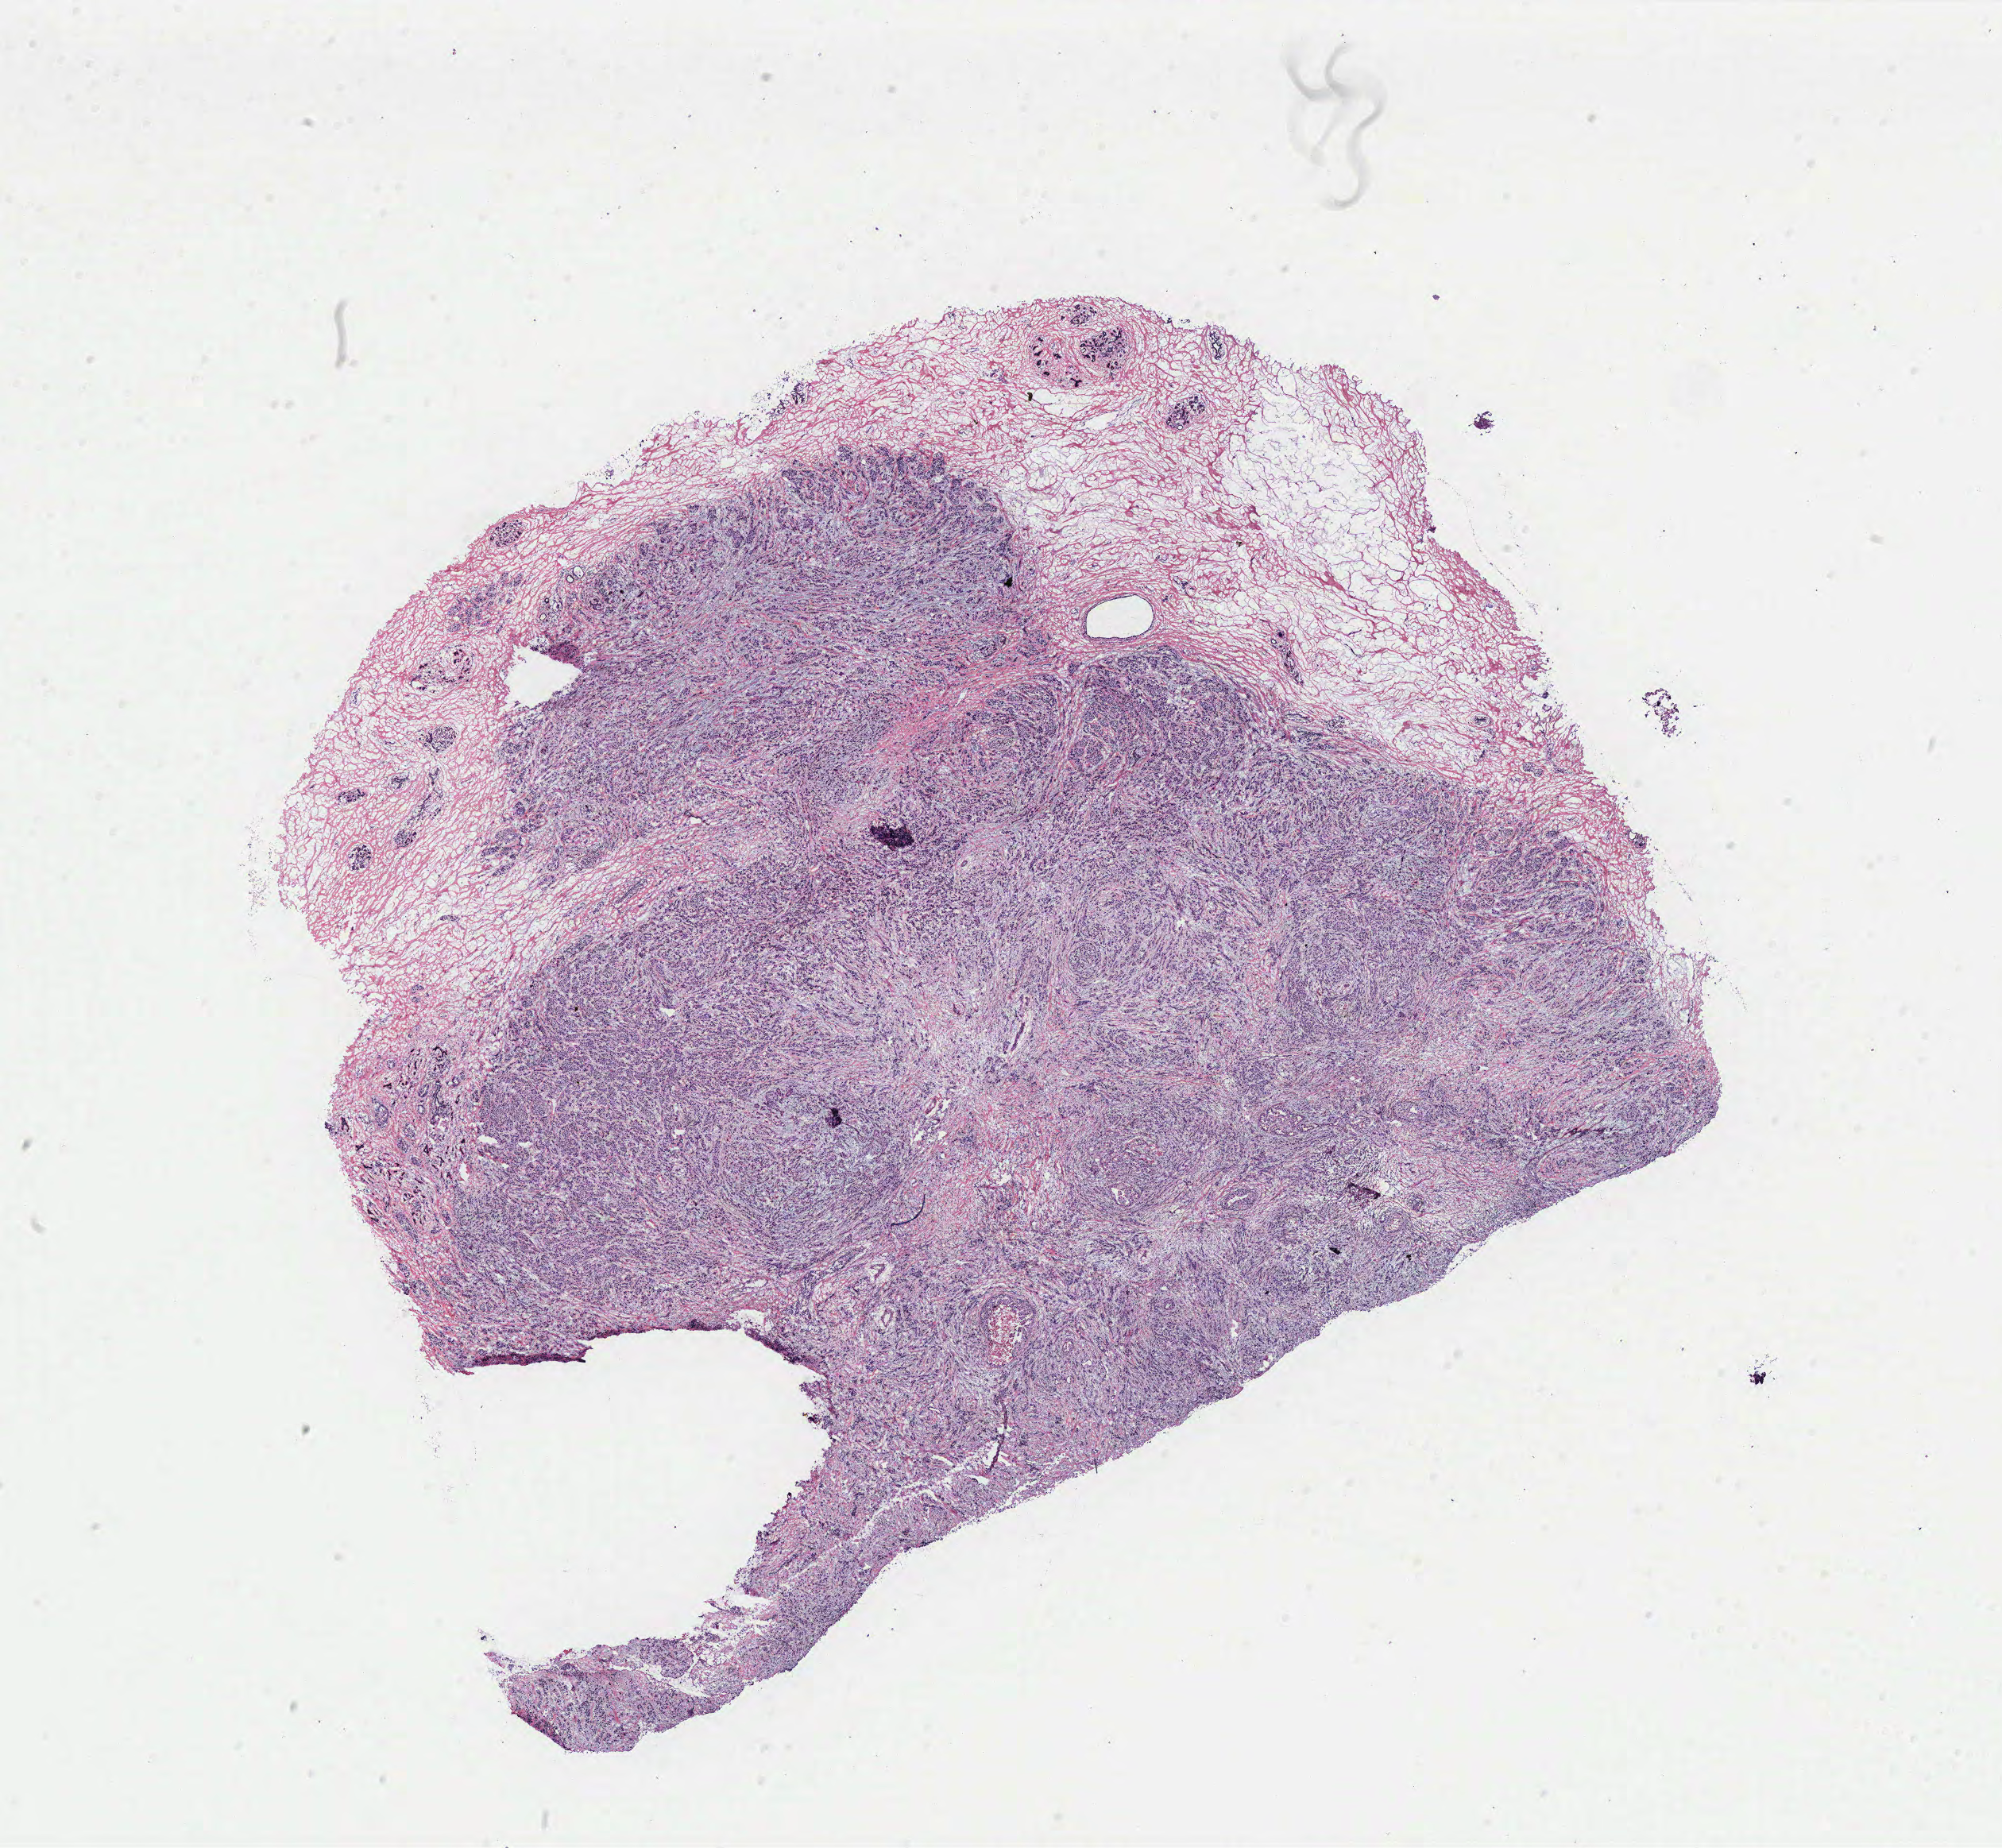
H&E whole-slide image — shown as a low-resolution overview of the whole scanned area (about 20.2 x 18.6 mm). Breast, tumour tissue. Female, 48 y/o.
Histologic diagnosis: Infiltrating duct carcinoma, NOS.